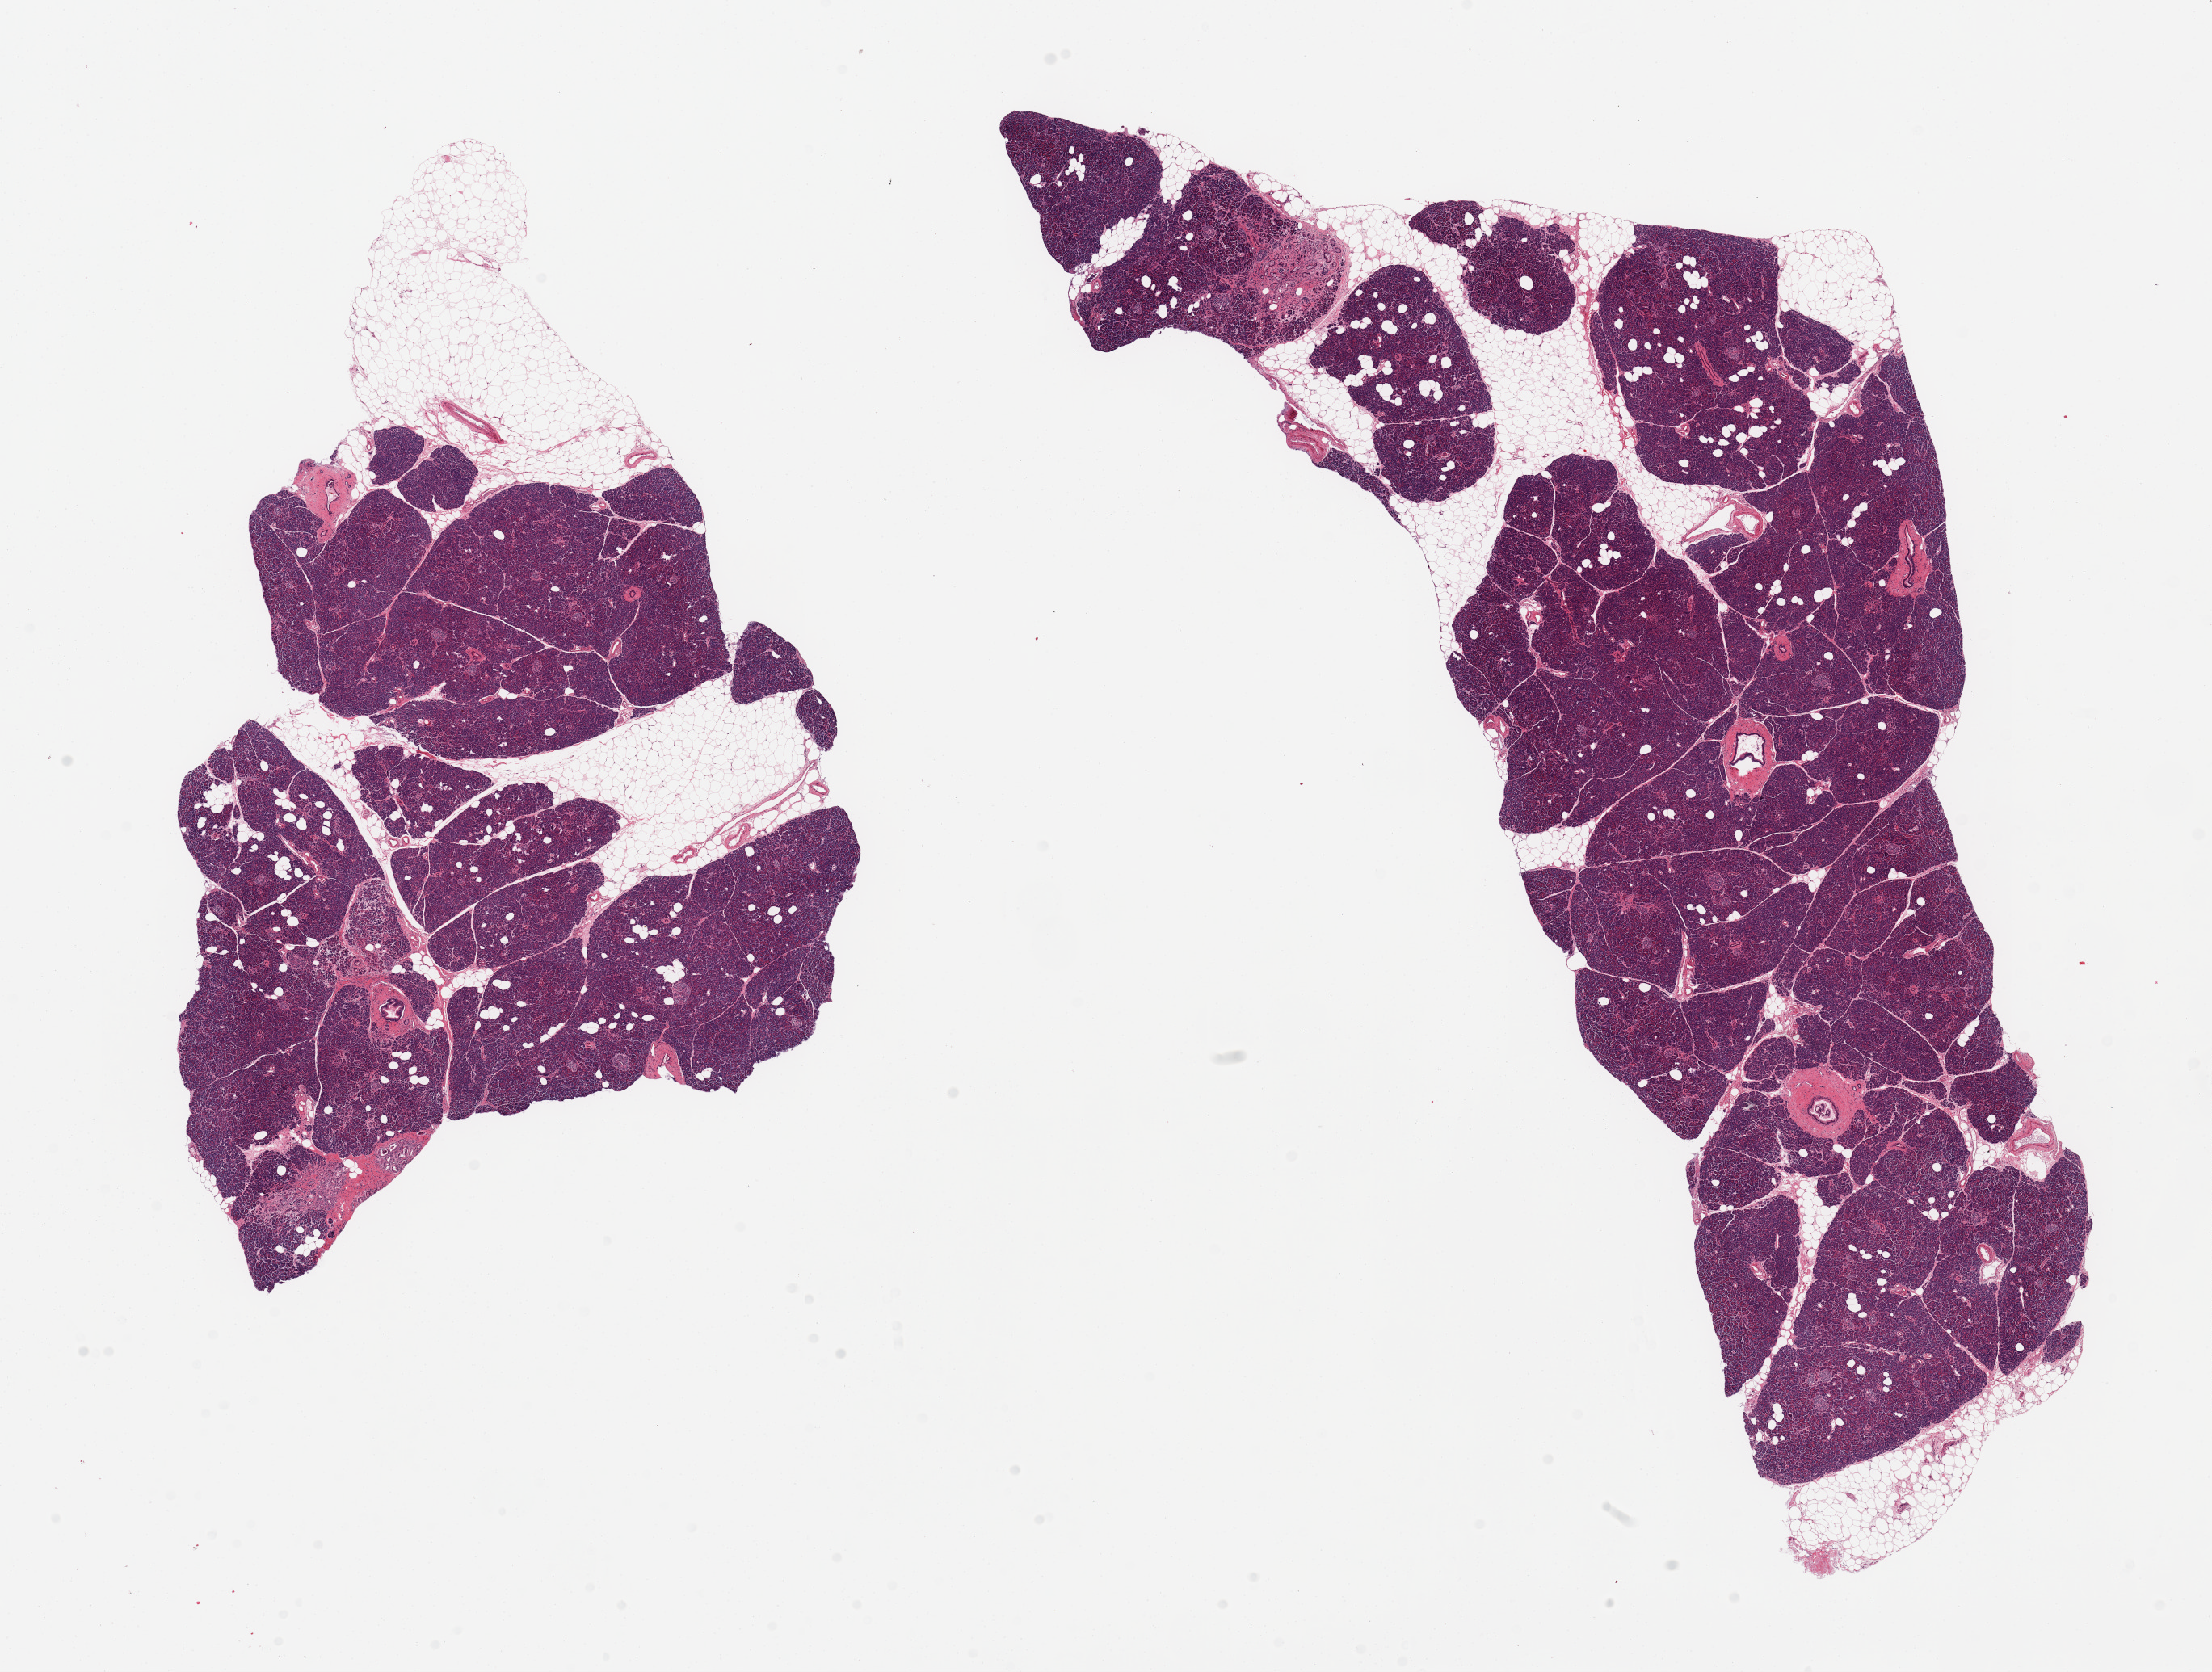
Hematoxylin and eosin (H&E) whole-slide image, brightfield, shown as a low-resolution overview of the whole scanned area (about 21.7 x 16.4 mm), PAXgene-fixed, paraffin-embedded tissue, target tissue: pancreas, donor tissue sample. Donor sex: male.
Reviewer comment on this tissue sample: 2 pieces; several small foci of exocrine atrophy; 40 & 20% internal & external fat.